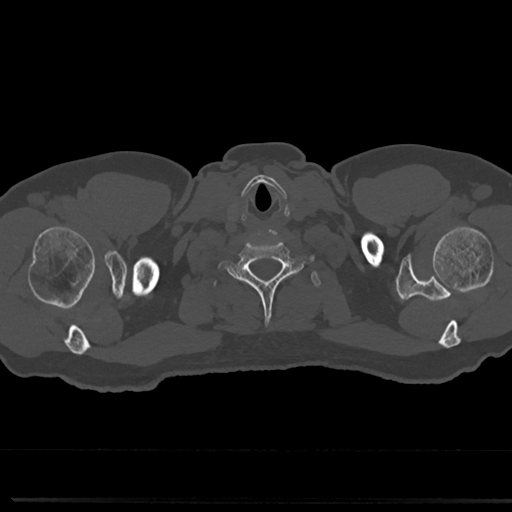
CT including the spine, one axial slice. Slice 703 of 817 in the series (ordered by position). Reconstruction kernel Br40s/3. Bone window (W 1800 / L 400 HU). 512 × 512 image matrix. Patient: male, 61 years. Case-level facts recorded for this patient, not image findings: primary cancer: prostate.
Annotated regions visible in this slice (semi-automatically segmented with operator editing):
- T1 vertebra: bounding box (x1, y1, x2, y2) in pixels: (209, 273, 317, 296)